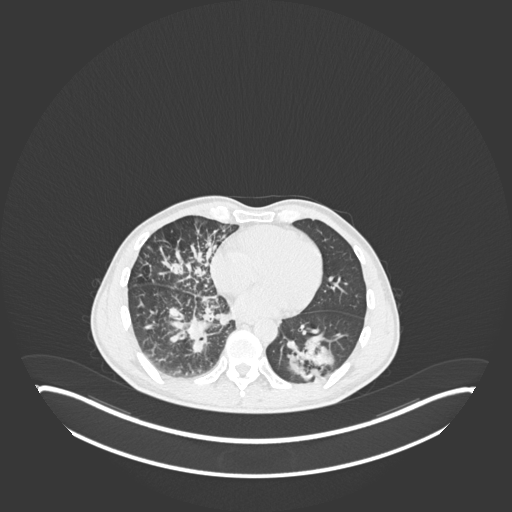
Chest CT, one axial slice; position 90 of 237 along the scan axis; reconstruction kernel B30f; 120 kVp; lung window (W 1500 / L -600 HU); 1 mm slice thickness; 512 × 512 image matrix. Patient: male, 49 years. From the clinical record (not read from this slice): clinical TNM (as recorded): T2b N1 M0.
Structures marked on this image (bounding box drawn by a radiologist):
- lung tumour (recorded histology: adenocarcinoma): bounding box <286,332,340,384> (left, top, right, bottom; pixels)